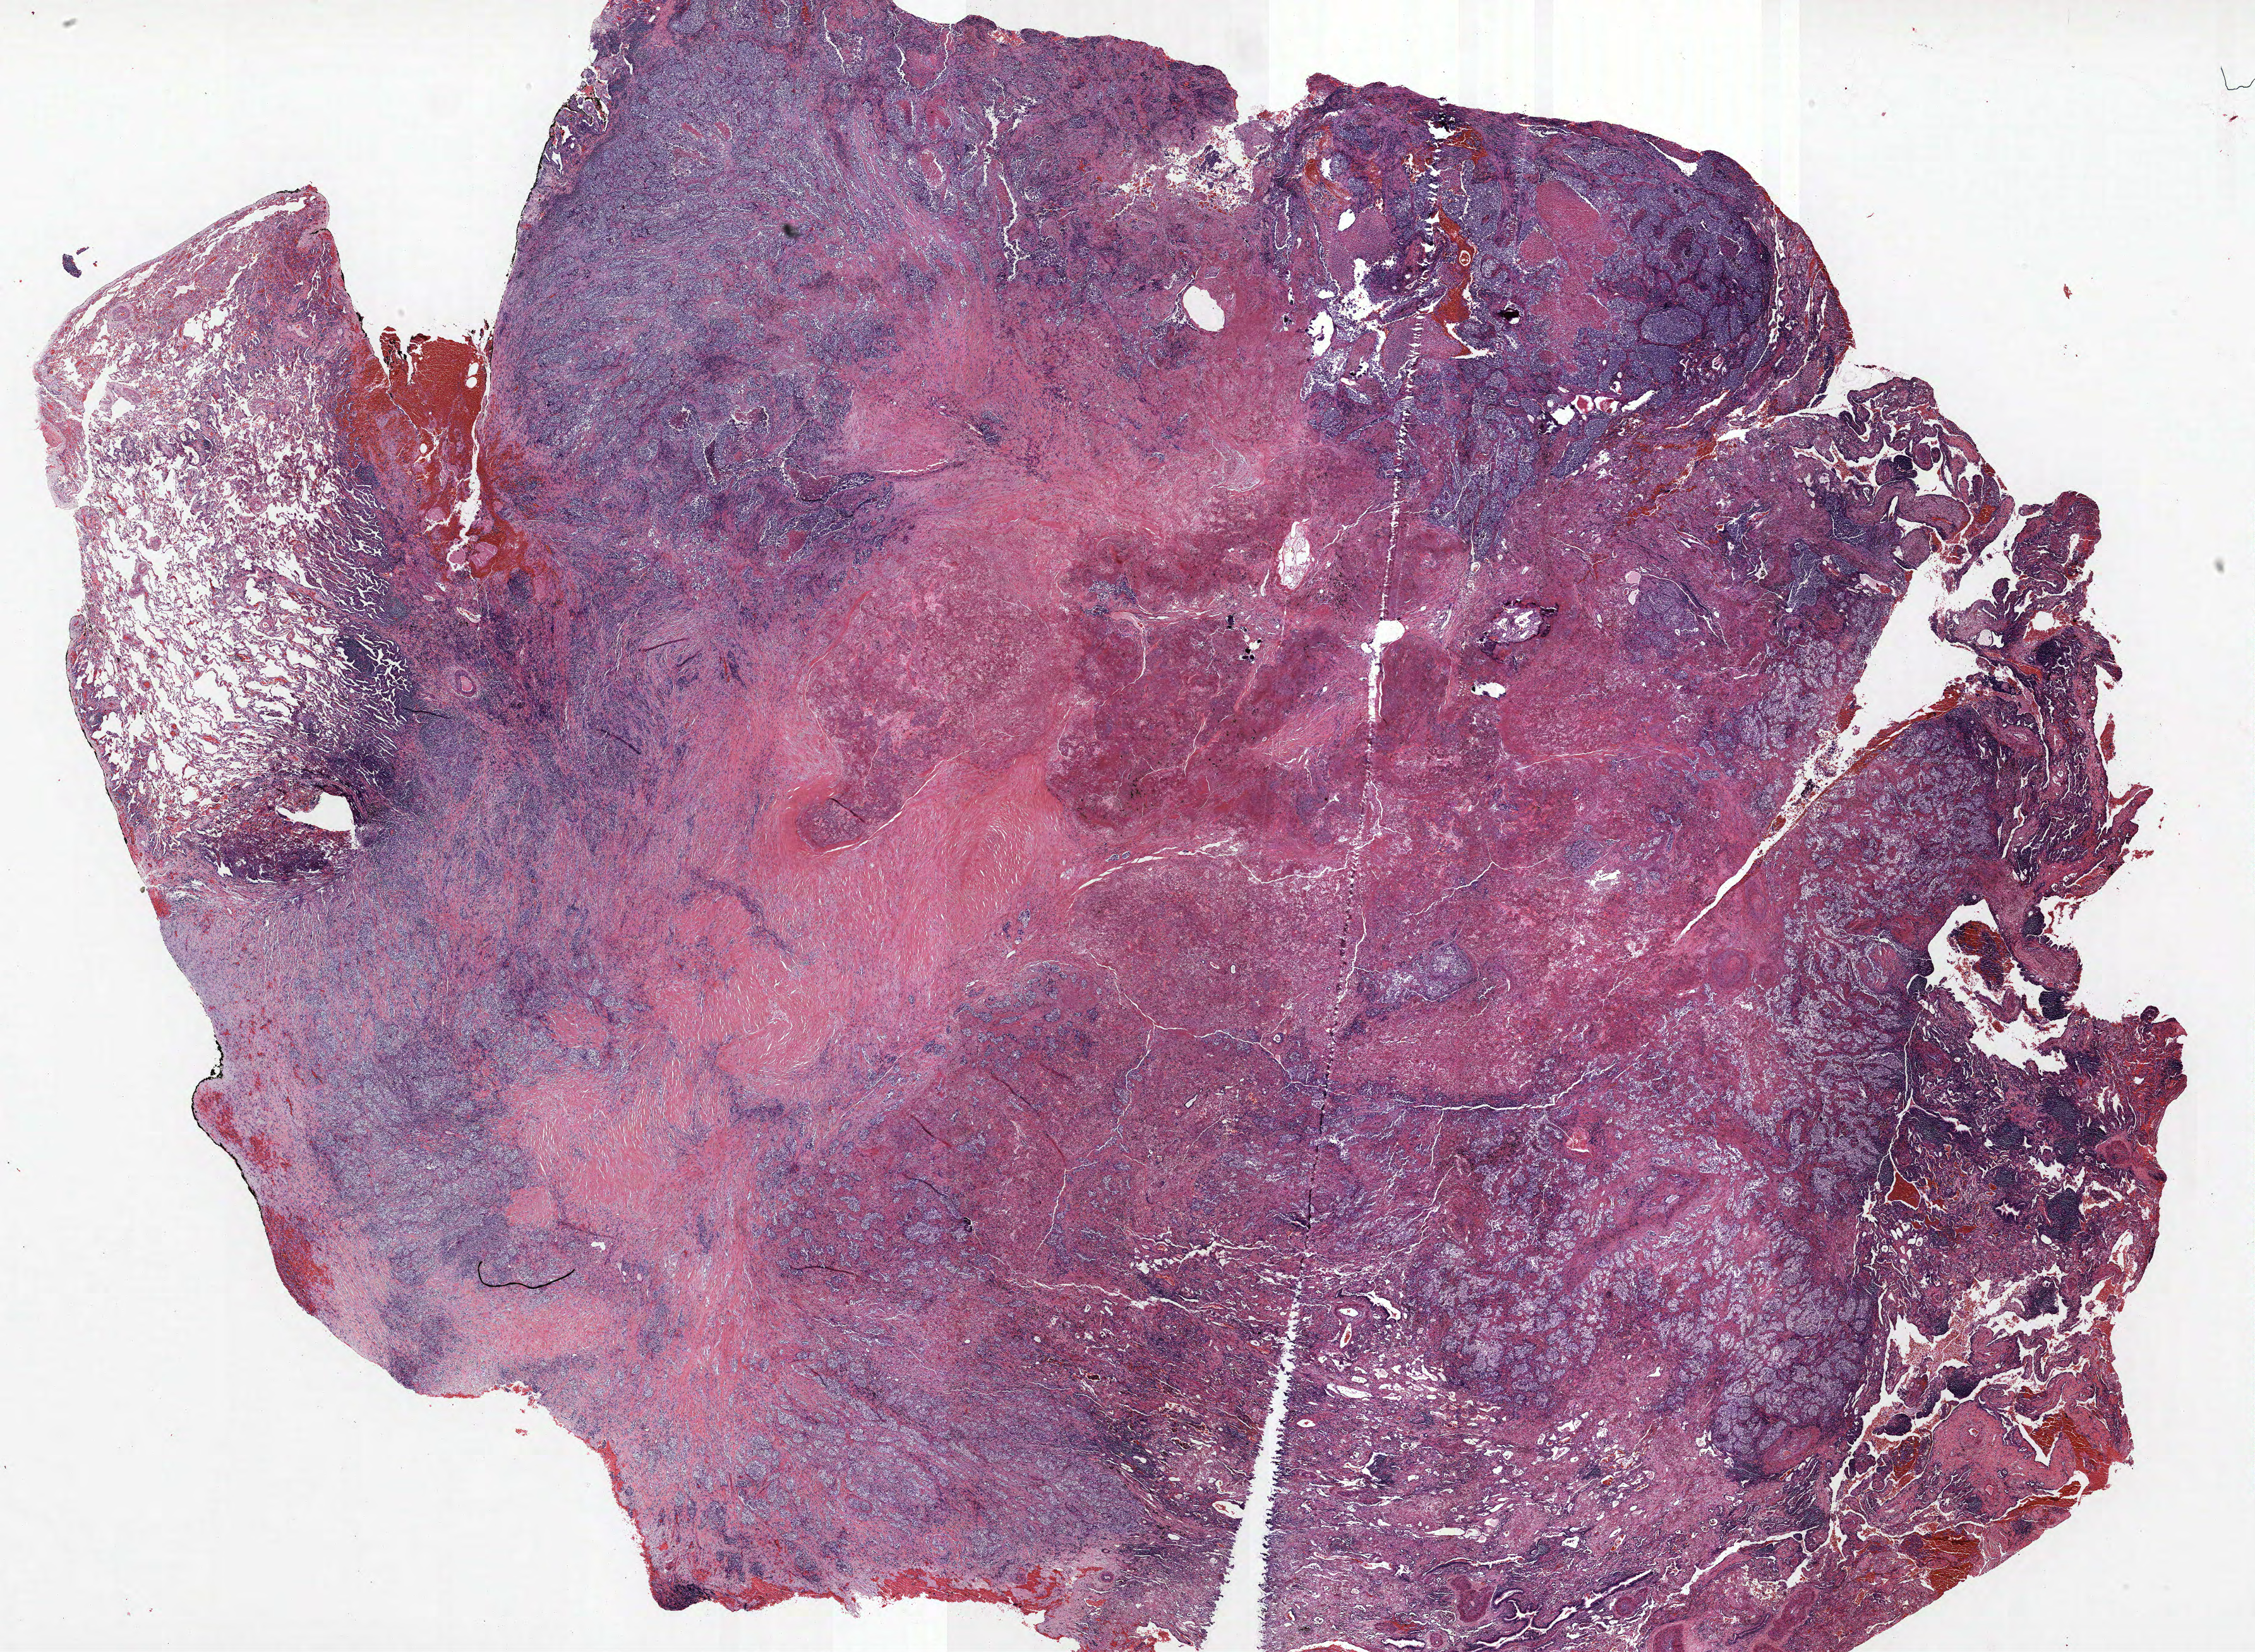
Whole-slide histology image, H&E-stained, a low-resolution overview of the entire scanned area, about 28.6 x 20.9 mm; formalin-fixed paraffin-embedded (FFPE) section; lung. Male, age 59 at enrolment. Former smoker at enrolment. Grade: undifferentiated (G4).
• tumour size (pathology): 25 mm
• primary tumour location (clinical record): right upper lobe
• participant's lung-cancer diagnosis: Large cell carcinoma, NOS (ICD-O-3 8012/3)
• stage (AJCC 6th edition): IA